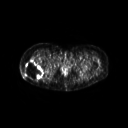
FDG PET of an extremity soft-tissue mass (from a PET/CT study), one axial slice. Slice 38 of 267 in the series (ordered by position). 128 × 128 image matrix, field of view 600 × 600 mm. Female patient, age 57 years. Case-level facts recorded for this patient, not image findings: histological type: epithelioid sarcoma with vascular differentiation; site of the primary tumour: right buttock.
Outlined on this slice (expert contour drawn on MRI and transferred to this co-registered scan by the dataset authors):
- gross tumour volume (mass): bounding box [x1, y1, x2, y2] px = [24, 59, 43, 80]